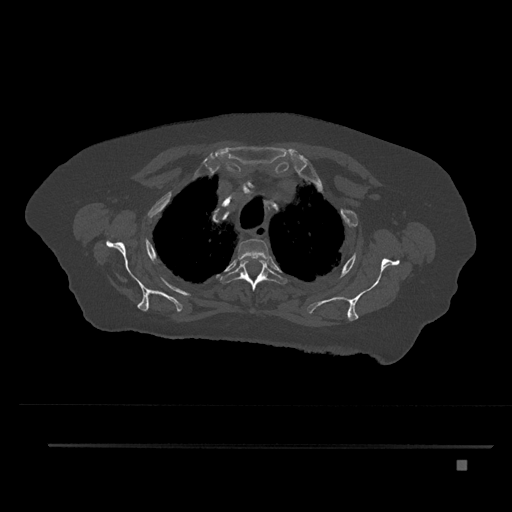
CT including the spine, one axial slice. Bone window (W 1800 / L 400 HU). 512 × 512 image matrix, field of view 437 × 437 mm. Patient: female, 76 years. From the clinical record (not read from this slice): primary cancer: lung; vertebrae with lytic lesions (as recorded): T11, L3.
Structures marked on this image (semi-automatic segmentation, software-assisted and operator-edited):
- T2 vertebra: bounding box (x1, y1, x2, y2) in pixels: (238, 239, 270, 262)
- T3 vertebra: (220, 257, 287, 291)